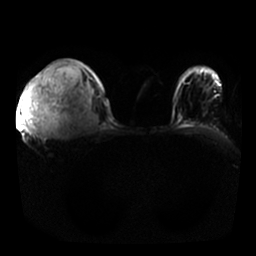
Breast MRI, one axial slice. Diffusion-weighted series; image 2 of 4 stored at this slice position (different b-values; order by instance number). 1.5 T. 4 mm slice thickness. 256 × 256 image matrix, field of view 350 × 350 mm. Female patient.
Annotated regions visible in this slice (expert manual segmentation):
- tumour on diffusion-weighted imaging: box from (x=23, y=61) to (x=70, y=128) px